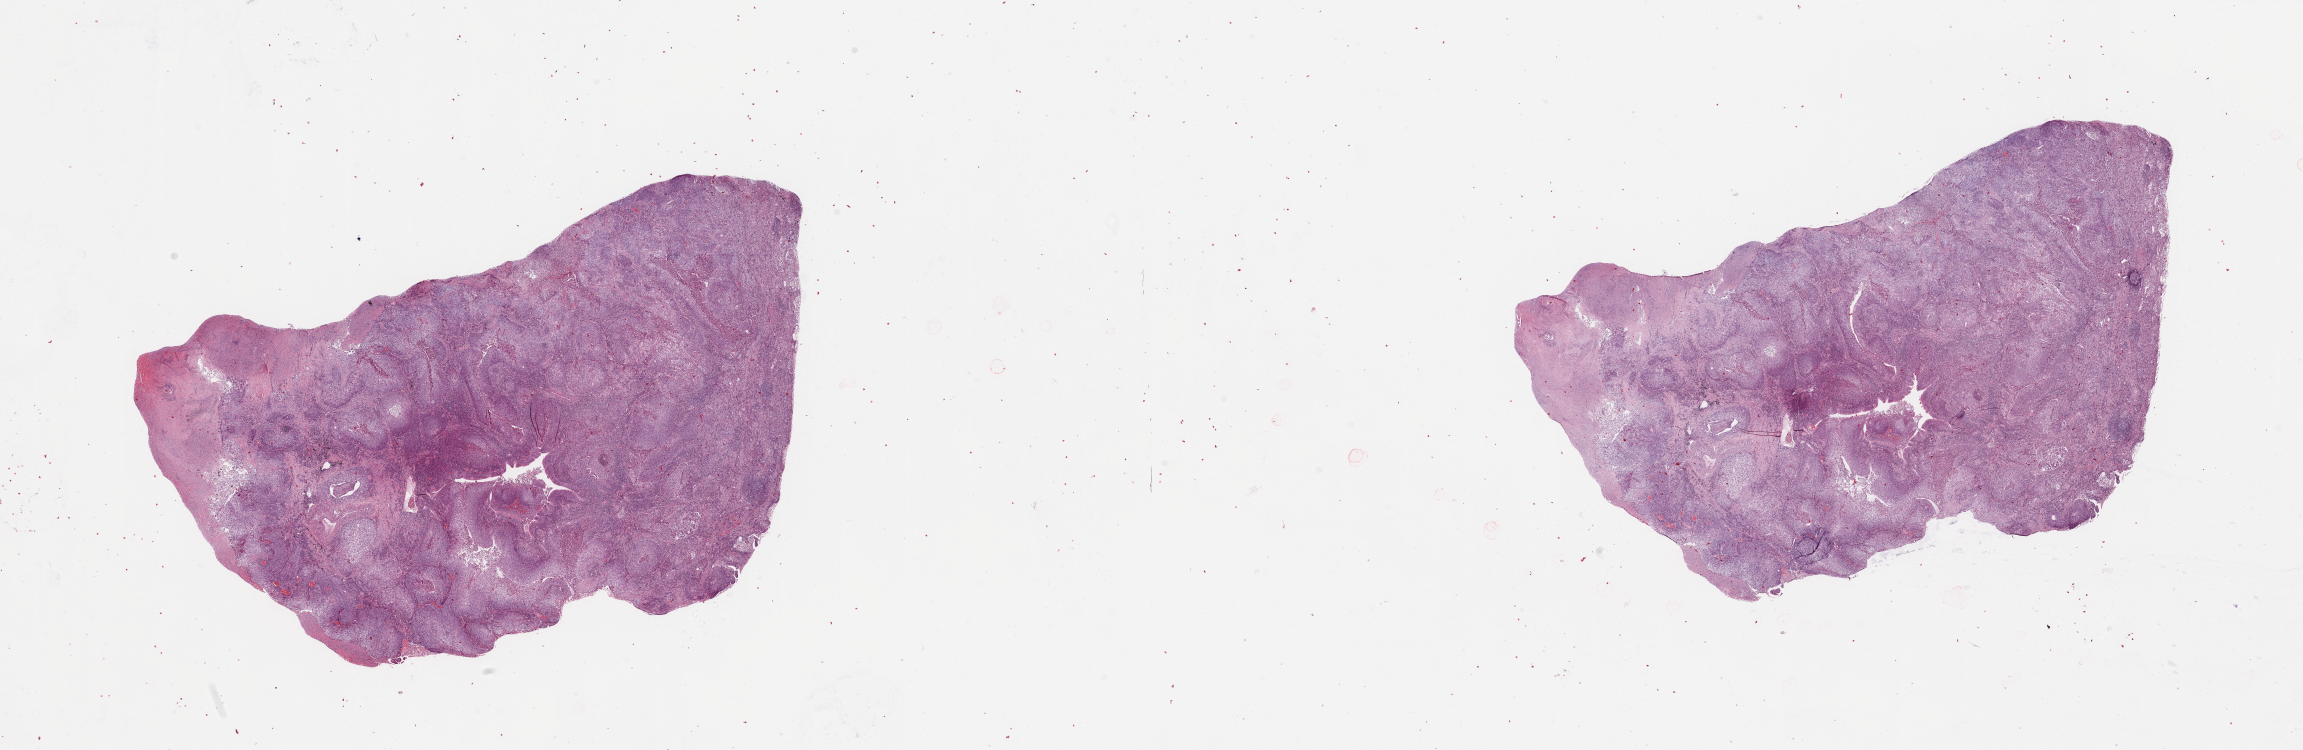
Hematoxylin and eosin (H&E) stained whole-slide image, shown as a low-resolution overview of the whole scanned area (about 36.4 x 11.9 mm, slide scanned at 20x), tumour tissue sample, sampled site: lung. 53-year-old male patient. Histologic grade: G2 (moderately differentiated). Composition of this section per pathologist review: tumour nuclei 65%, necrosis 15%.
Histologic diagnosis: Squamous cell carcinoma, NOS. AJCC pathologic stage: IIIA.